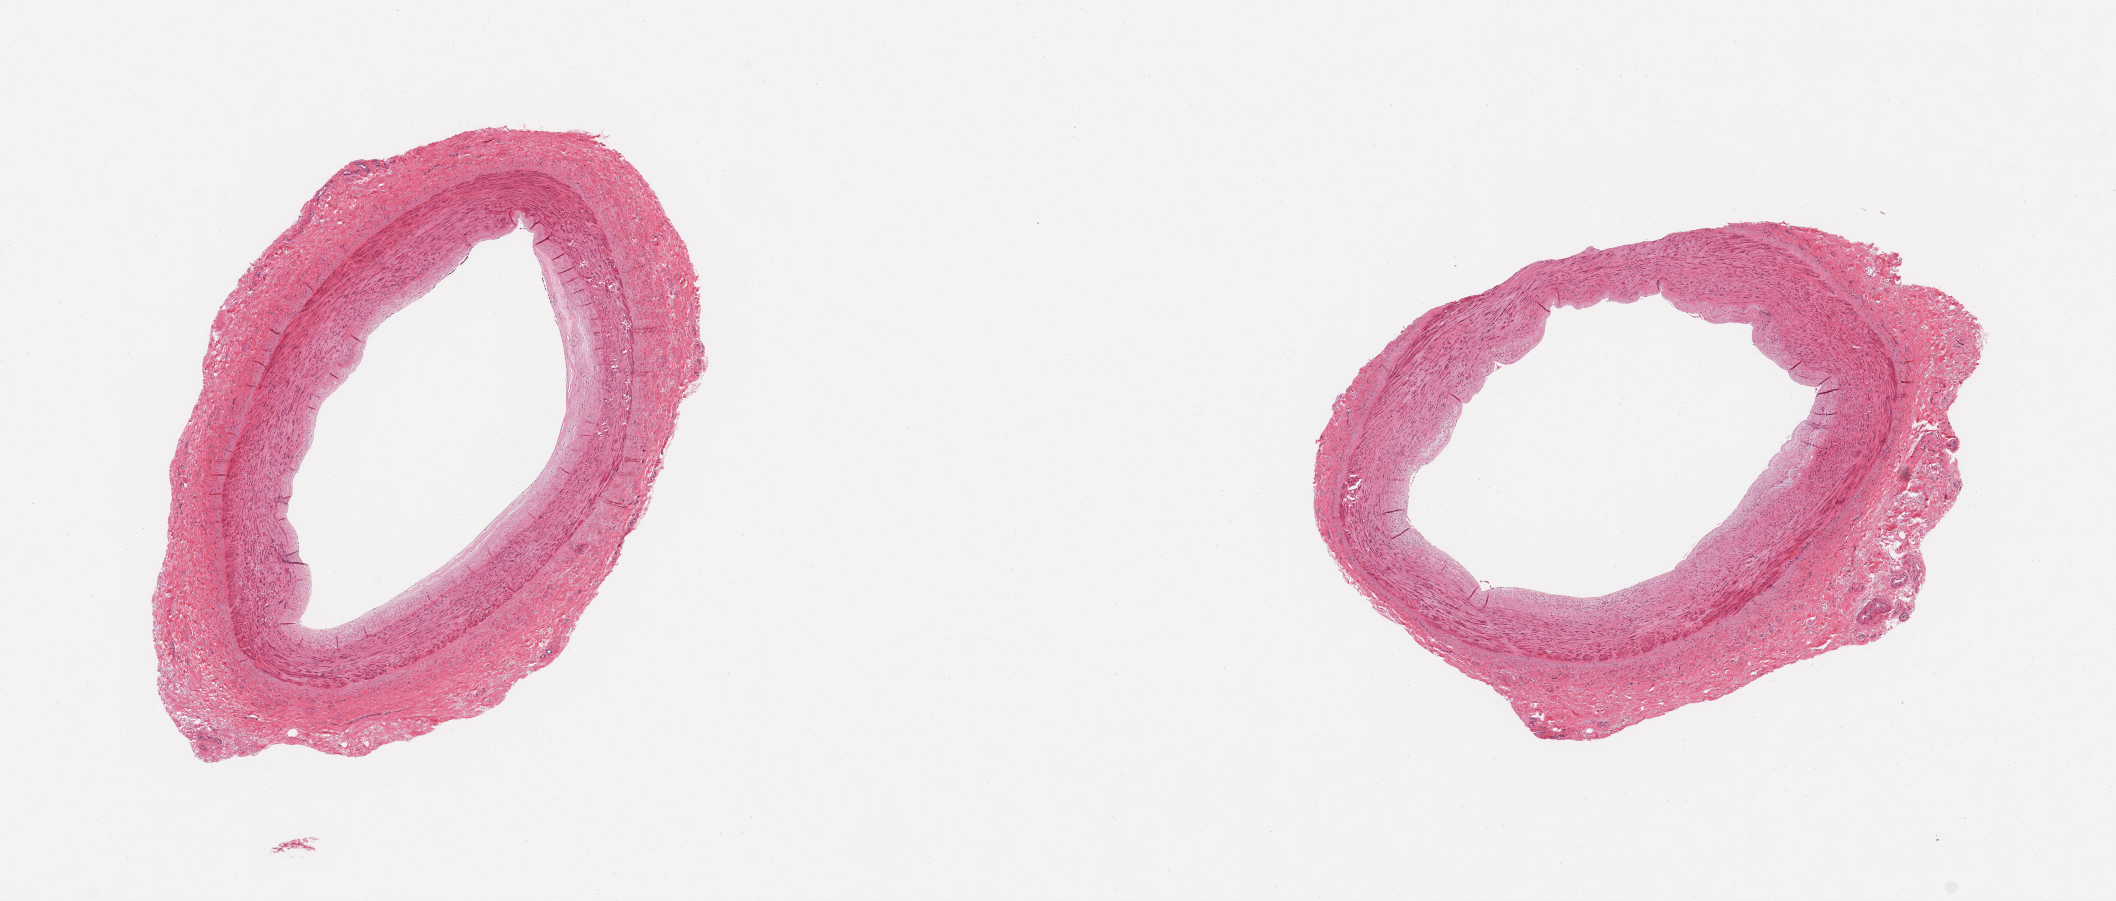
Haematoxylin and eosin whole-slide image — a low-resolution overview of the entire scanned area, about 16.7 x 7.1 mm, PAXgene-fixed paraffin-embedded (PFPE) section, section of tibial artery (target tissue), donor tissue sample. Male donor.
Reviewer comment on this tissue sample: 2 pieces, no atherosis; rims of fibrous tissue, ~0.5-1mm.